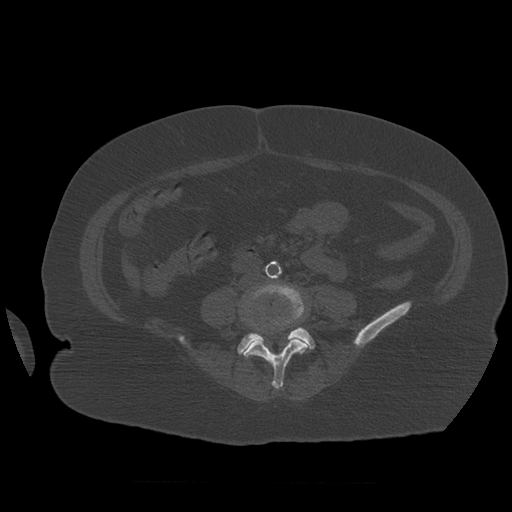
CT including the spine, one axial slice; slice 196 of 399 in the series (ordered by position); reconstruction kernel STANDARD; bone window (W 1800 / L 400 HU); 1.25 mm slice thickness; 512 × 512 image matrix, field of view 404 × 404 mm. Patient age 81 years. From the clinical record (not read from this slice): primary cancer: renal.
Structures marked on this image (semi-automatically segmented with operator editing):
- L4 vertebra: box from (x=242, y=283) to (x=310, y=389) px
- L5 vertebra: (x=238, y=323)–(x=316, y=355)